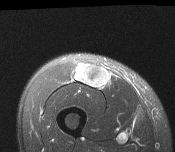
MRI of an extremity soft-tissue mass, one axial slice; T2-weighted fat-saturated; MR volume resampled by the dataset authors to the PET/CT grid (not the native acquisition matrix); 3.27 mm slice thickness; 175 × 152 image matrix, field of view 171 × 148 mm. Male patient. From the clinical record (not read from this slice): histological type: pleiomorphic leiomyosarcoma; grade: intermediate; site of the primary tumour: right thigh.
Outlined on this slice (expert contour drawn on MRI and transferred to this co-registered scan by the dataset authors):
- gross tumour volume including surrounding oedema: bounding box (x1, y1, x2, y2) in pixels: (76, 63, 109, 87)